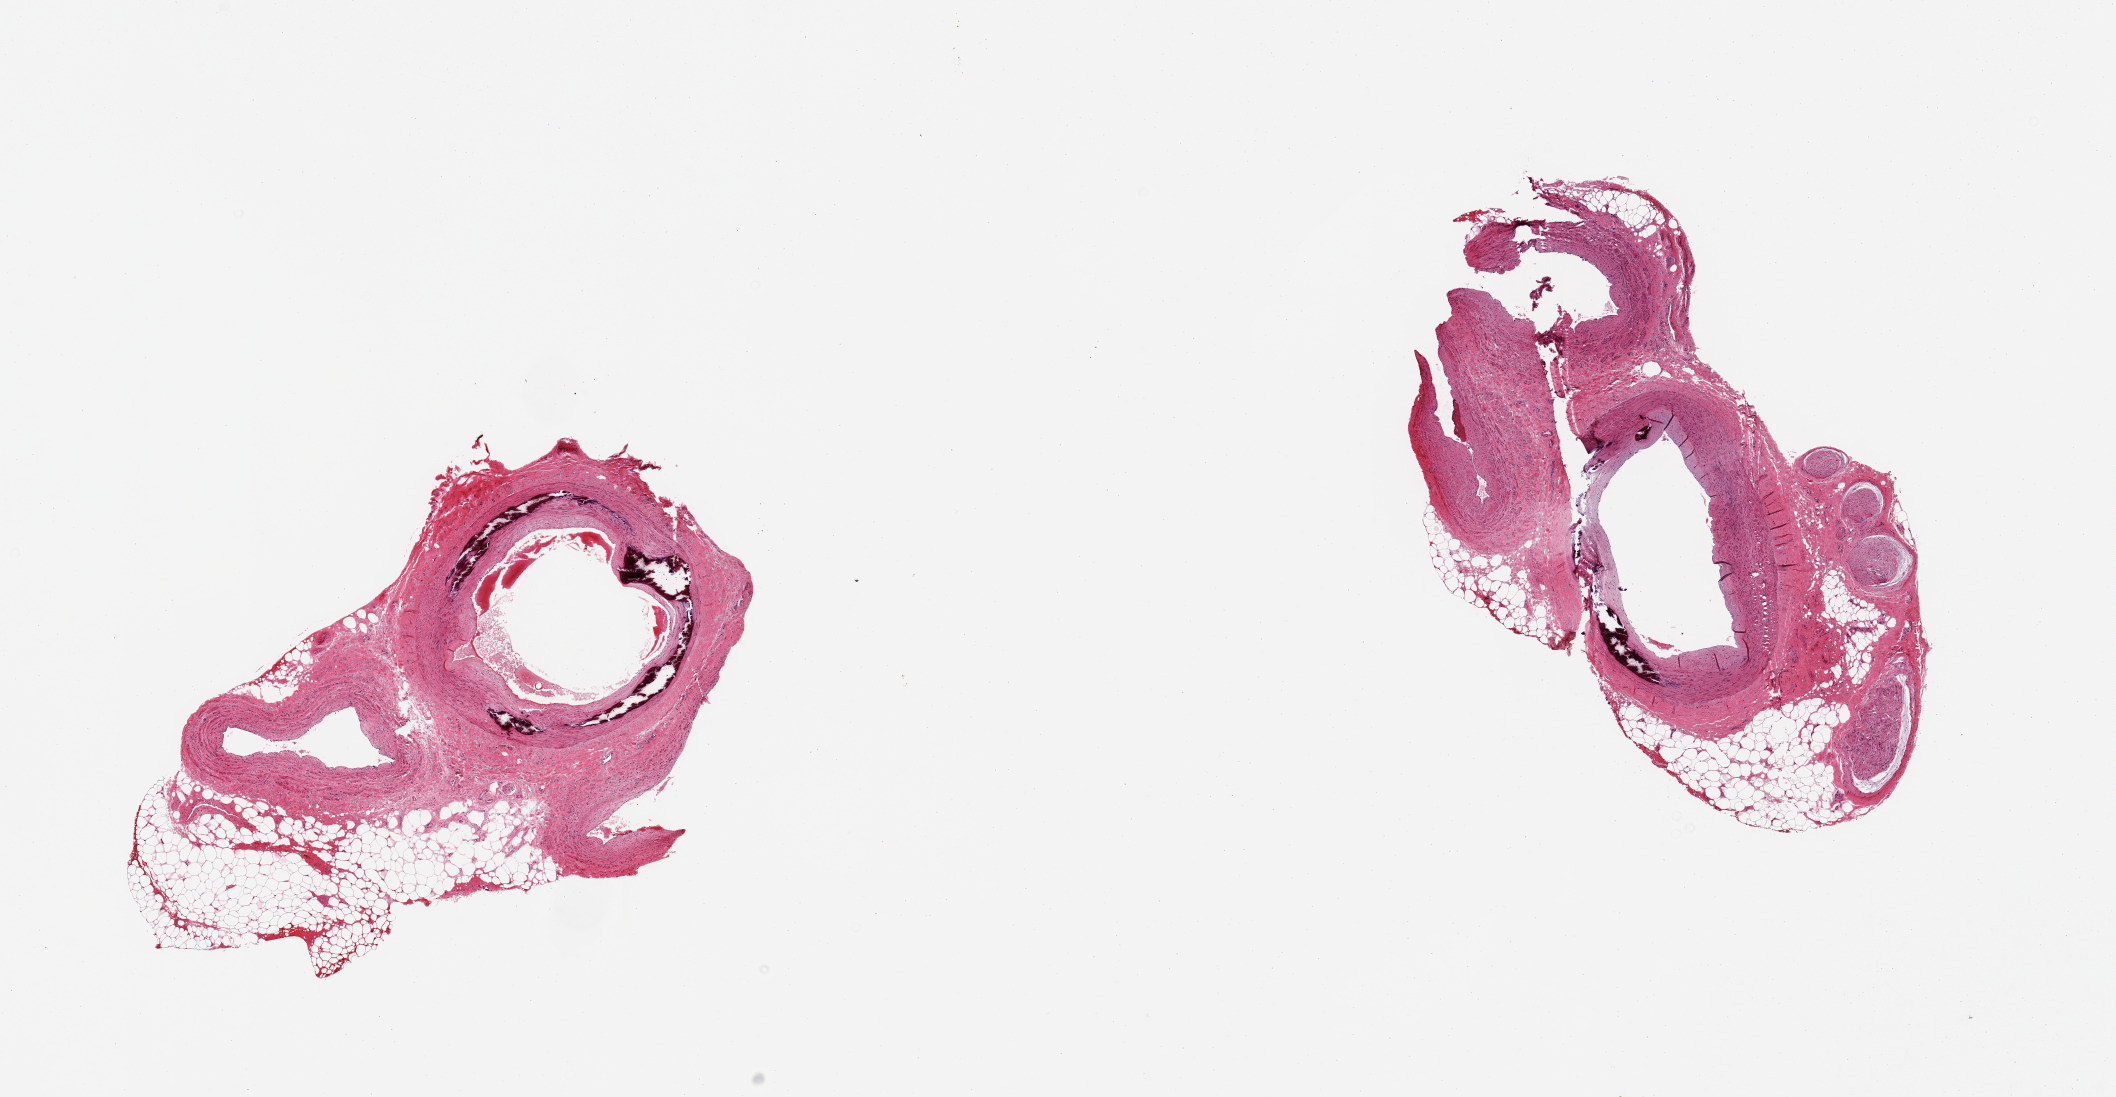
Haematoxylin and eosin whole-slide image — shown as a low-resolution overview of the whole scanned area (about 16.7 x 8.7 mm, acquisition: 20x scan), PAXgene-fixed paraffin-embedded (PFPE) section, section of tibial artery (target tissue), tissue donor sample. Donor: male.
* reviewer comment on this tissue sample: 2 pieces; heavily calcified but patent arteries; 30% external fatty & neural content